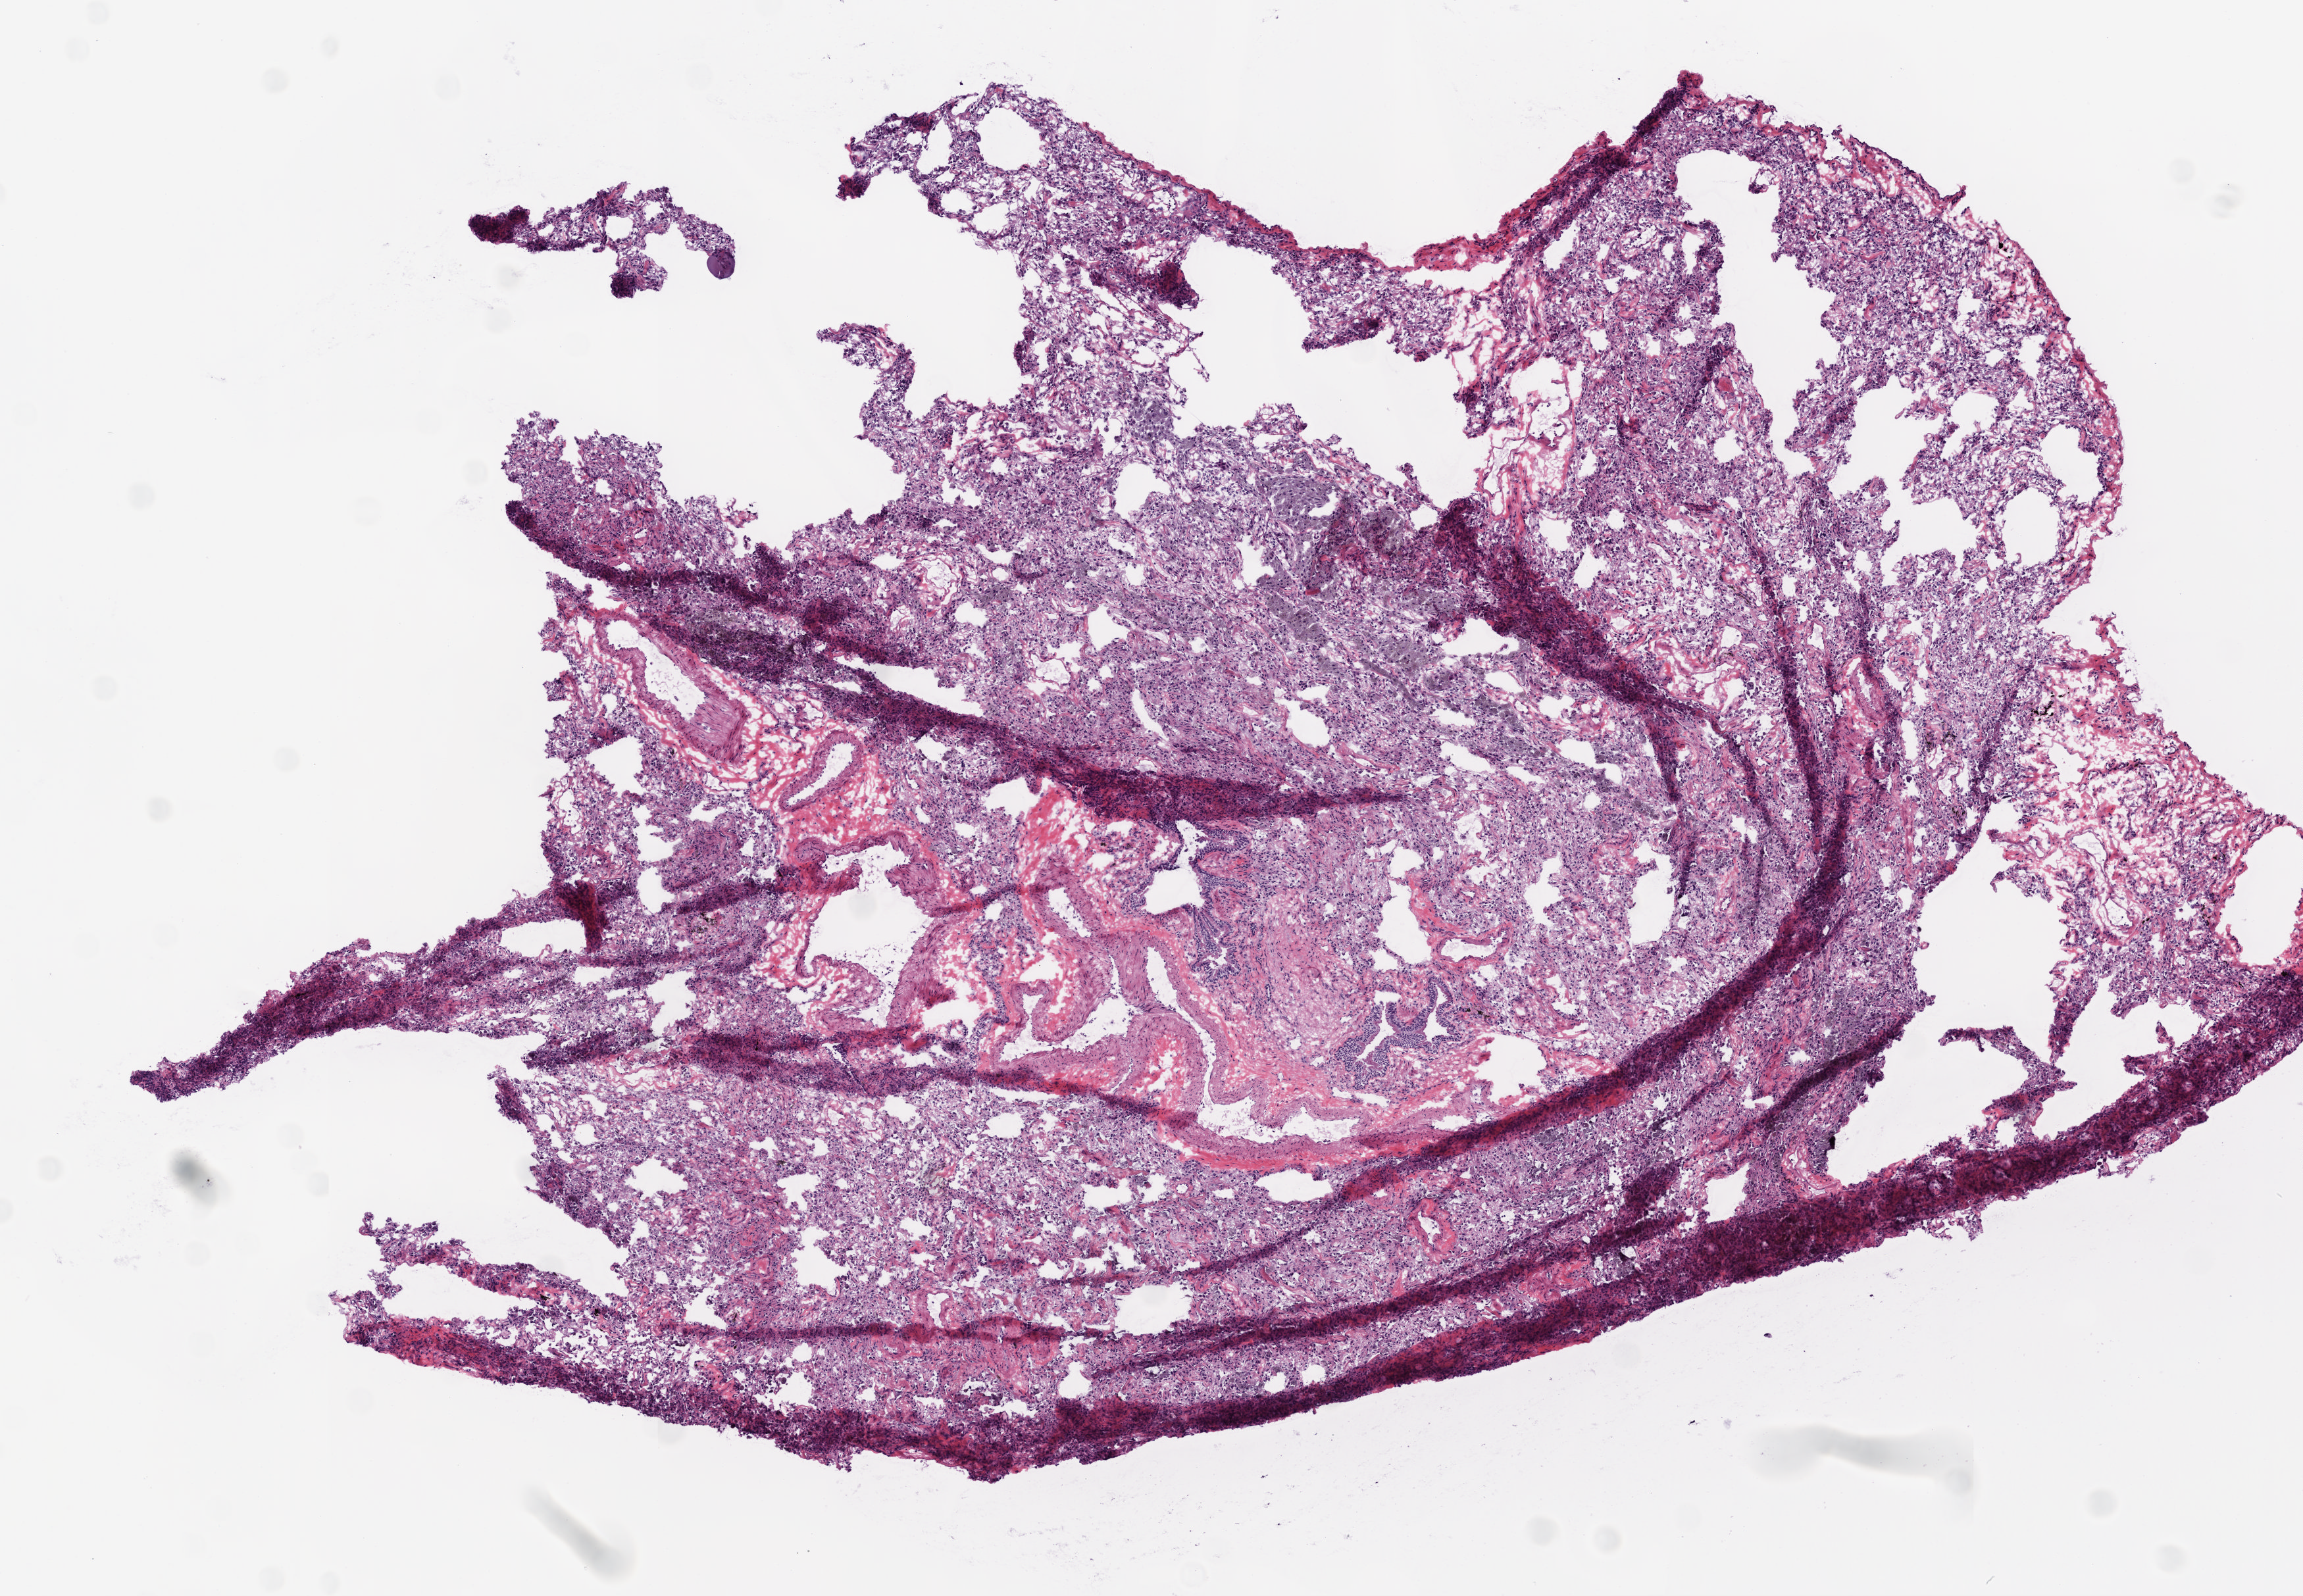
H&E whole-slide image — whole scanned area (about 7.0 x 4.9 mm, slide scanned at 20x) shown as a low-resolution overview, frozen section, solid tissue normal (non-tumour tissue) sample from the lung. Female, age 68 years at initial diagnosis.
This section: solid tissue normal (non-tumour) sample from the same patient. Patient diagnosis: Squamous cell carcinoma, NOS (upper lobe, lung).